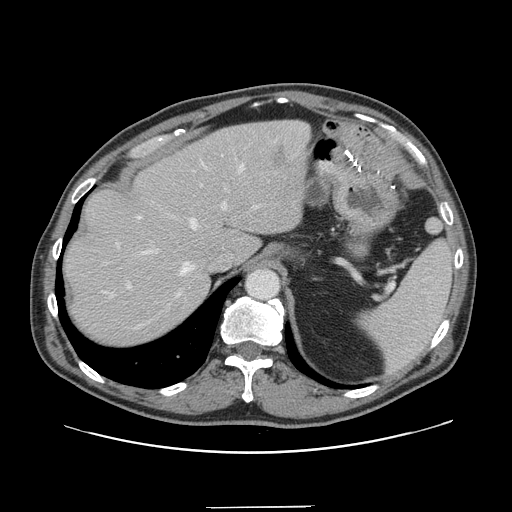
Contrast-enhanced abdominal CT, one axial slice. Intravenous contrast given. Soft-tissue window (W 400 / L 40 HU). 2.5 mm slice thickness. 512 × 512 image matrix, field of view 397 × 397 mm. Male patient, age 64 years. From the clinical record (not read from this slice): diagnosis: colorectal cancer liver metastases, imaged before liver resection; multiple liver metastases: yes; largest metastasis: 3.5 cm; disease in both lobes: yes.
Outlined on this slice (manually delineated by an expert):
- hepatic veins: bounding box [x1, y1, x2, y2] px = [143, 164, 244, 297]
- liver: [64, 121, 311, 345]
- planned liver remnant (the part of the liver to remain after resection): [64, 123, 269, 345]
- portal vein (with intrahepatic branches): [117, 155, 258, 289]
- liver metastasis: [275, 148, 287, 168]